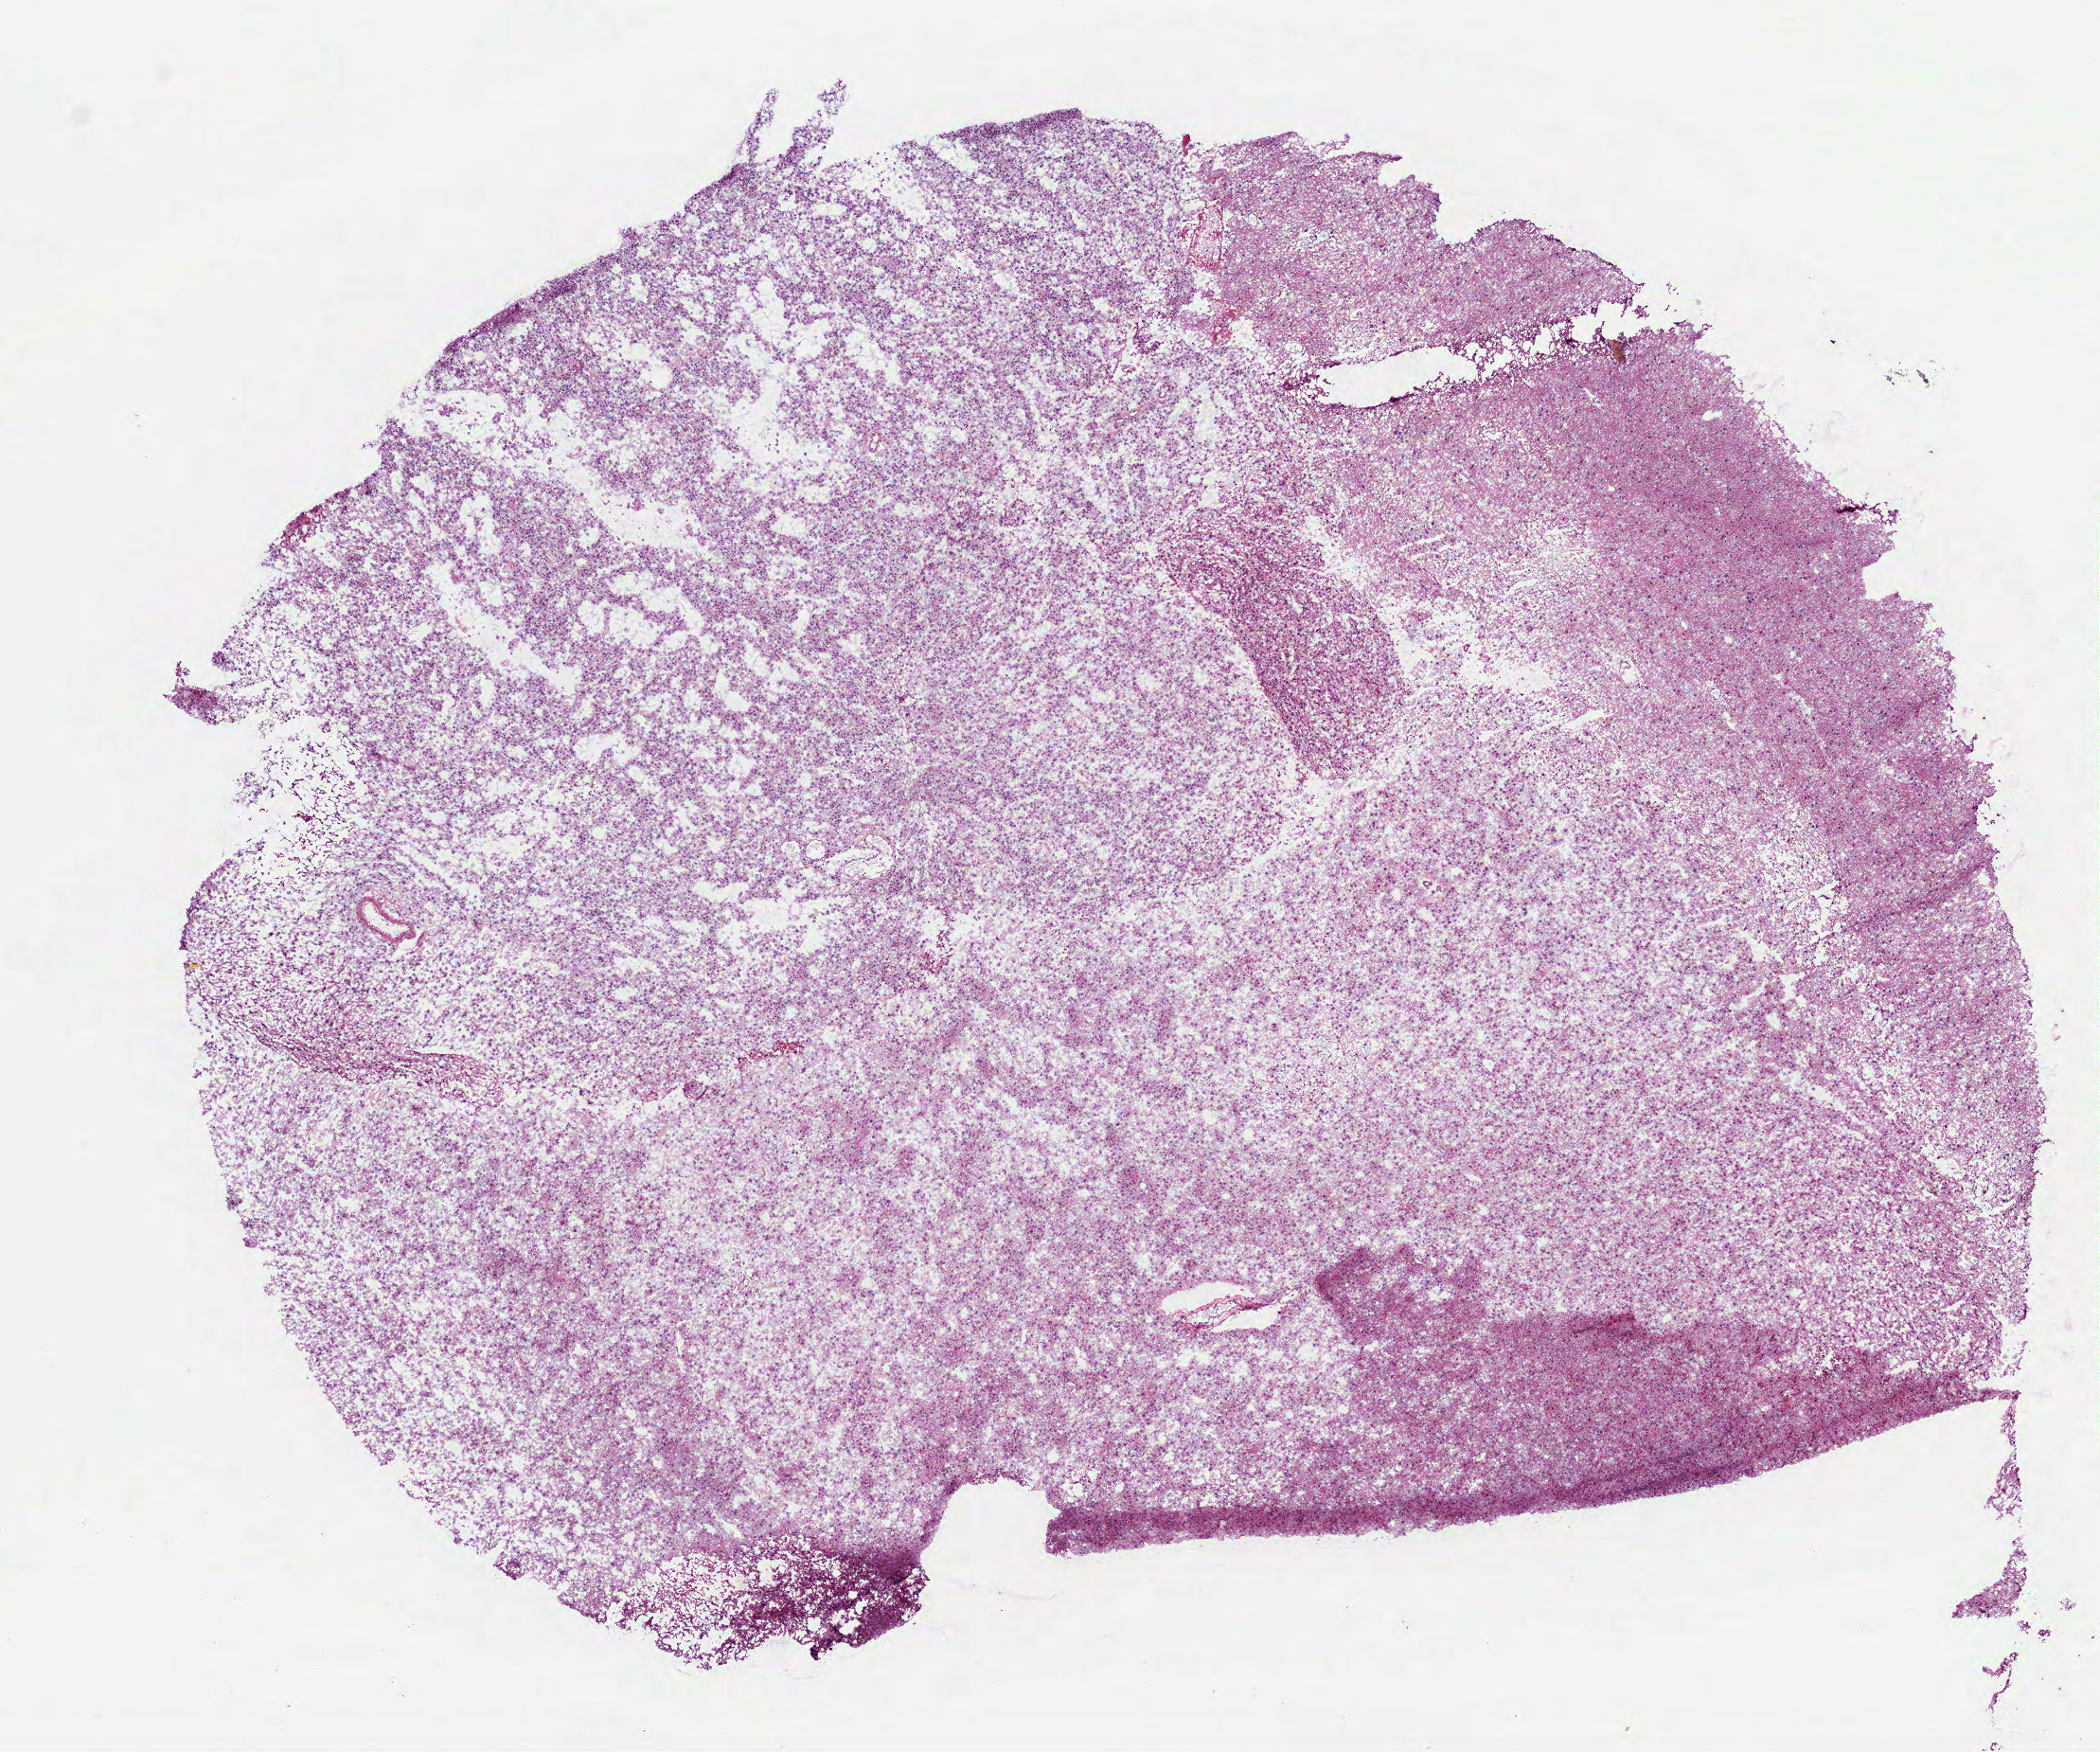
Hematoxylin and eosin (H&E) stained whole-slide image — a low-resolution overview of the entire scanned area, about 8.9 x 7.5 mm, frozen section from the top of the tissue portion, primary tumour sample from the brain. Male patient; age at initial diagnosis 53 years. Histologic grade: G2 (moderately differentiated). Slide review estimates, as recorded: tumour cells 100%, tumour nuclei 75%, normal cells 0%, stromal cells 0%, necrosis 0%.
Laterality: left. Diagnosis: Oligodendroglioma, NOS (cerebrum).